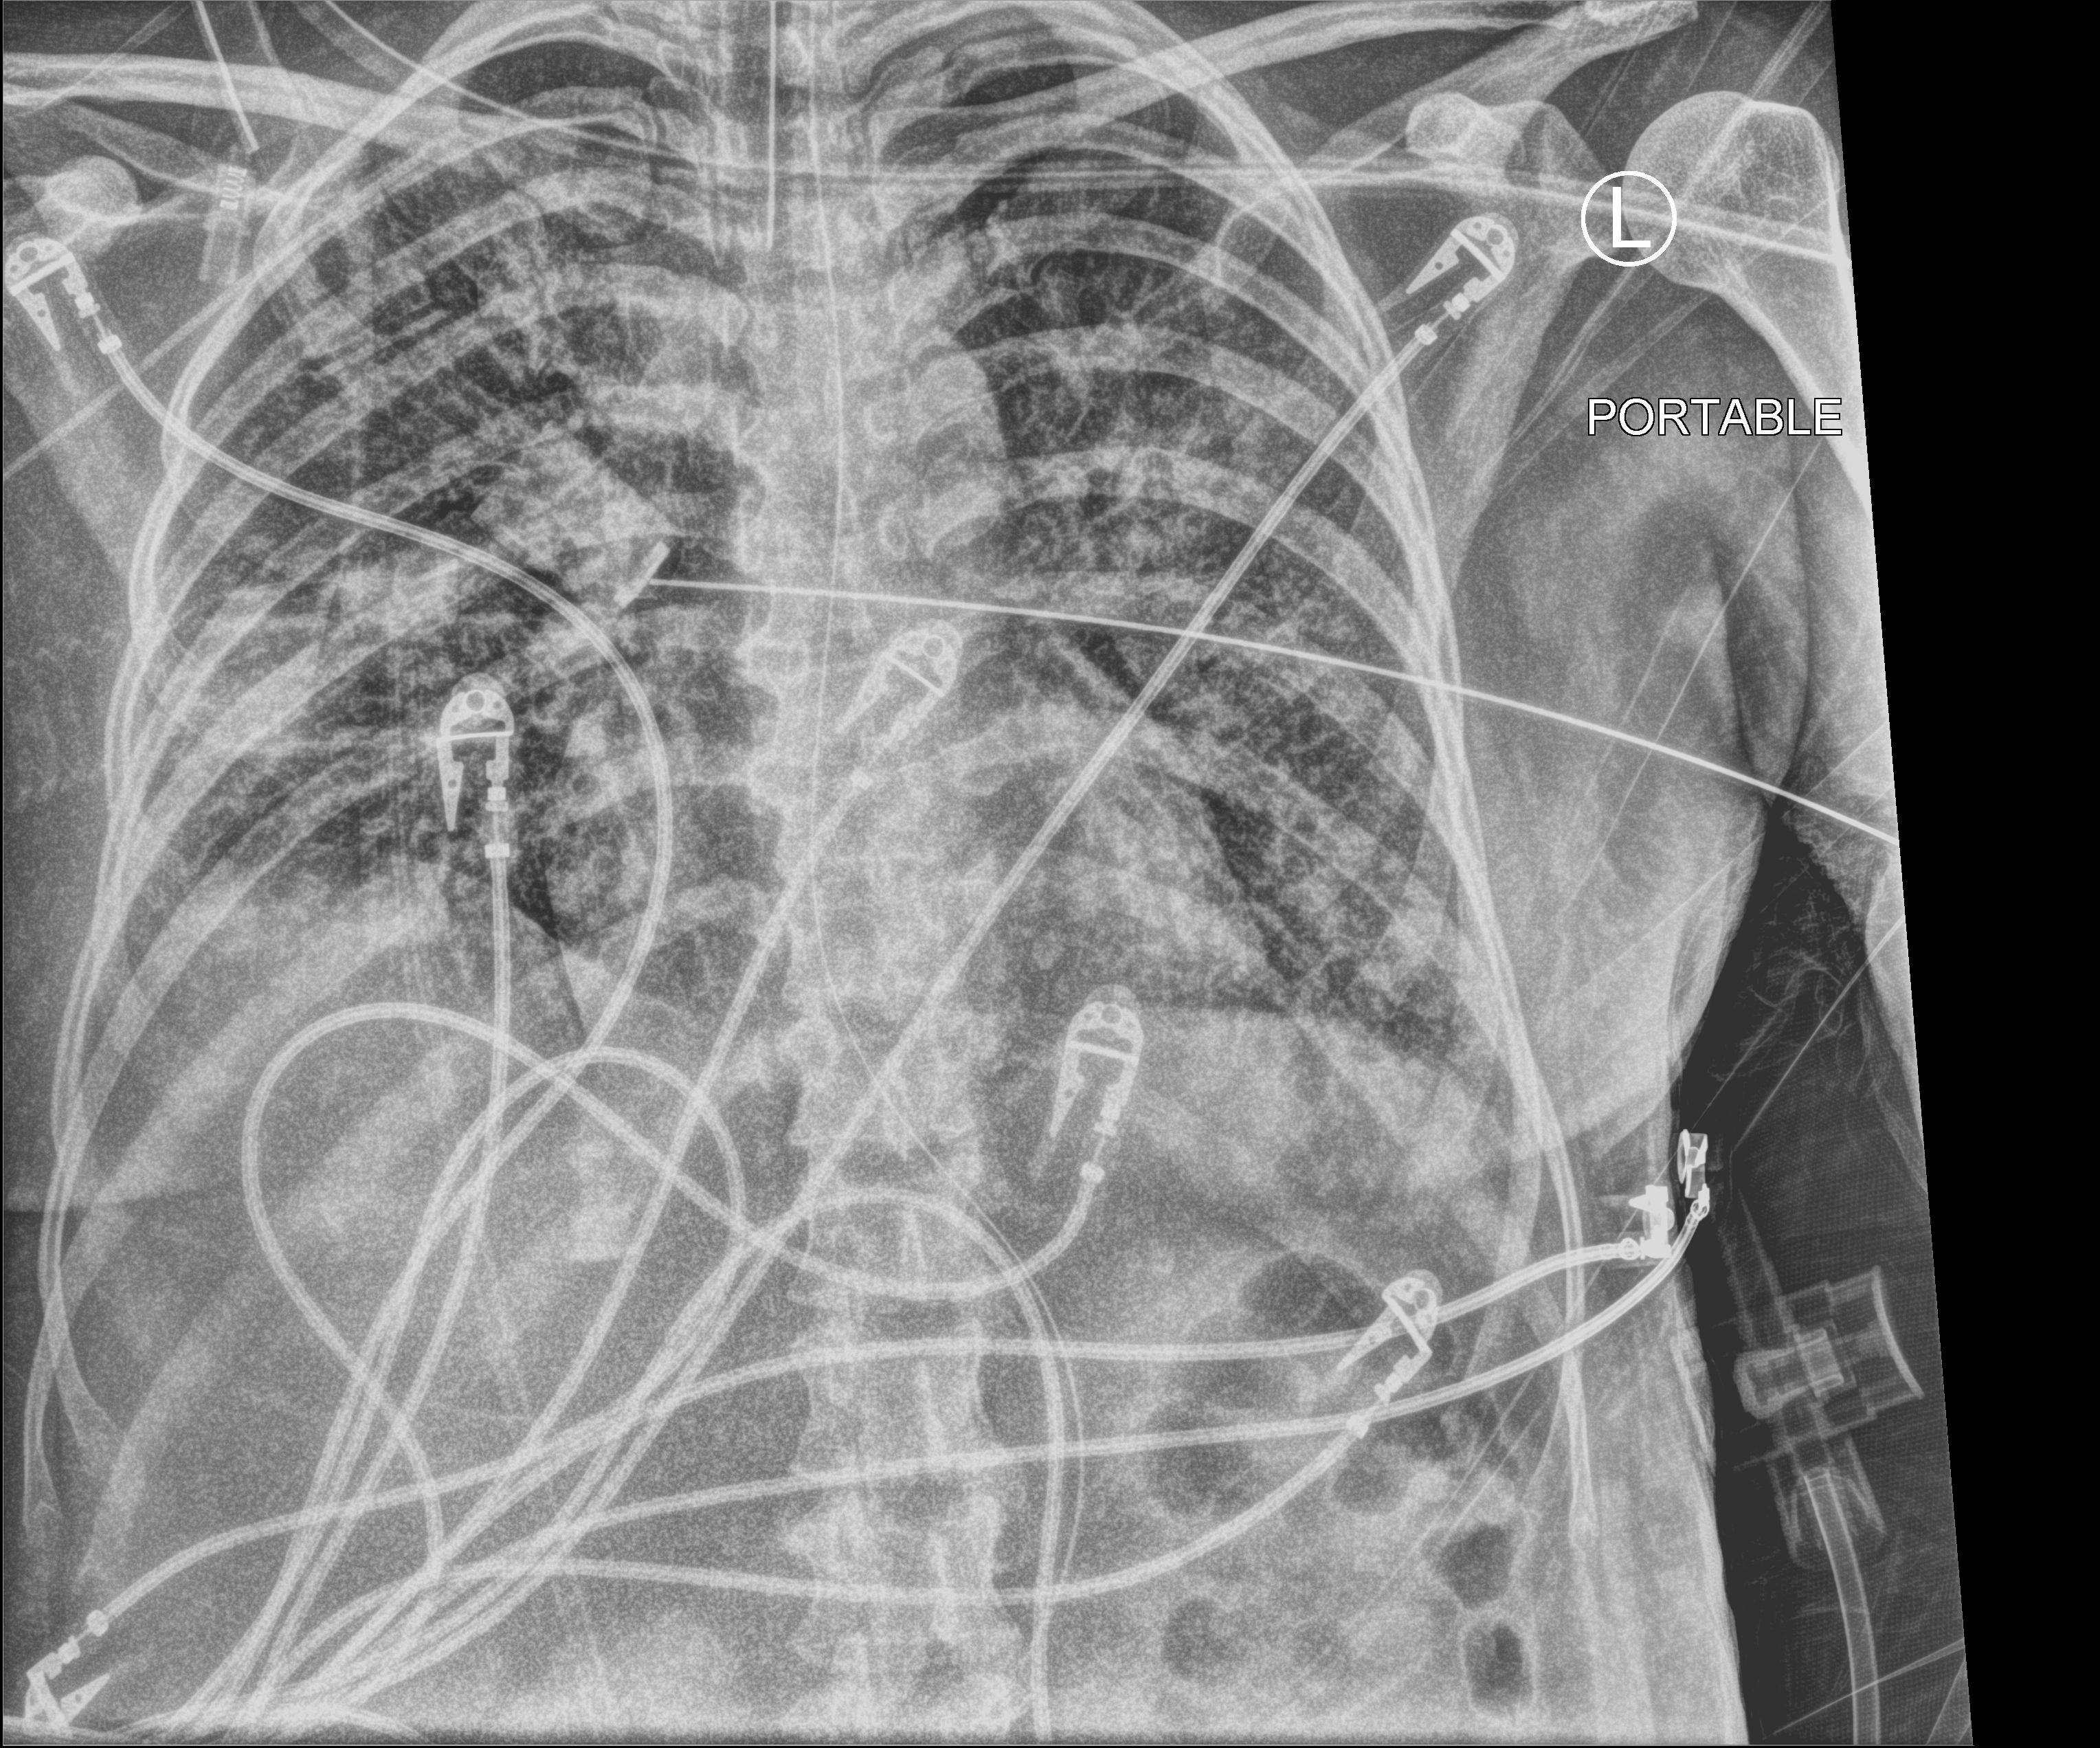
Bedside chest radiograph (computed radiography); anteroposterior (AP) projection. Female patient hospitalised with COVID-19, age 18–59 years.
Admission-level facts for this patient (not findings on this image; timing relative to this image not recorded):
- mechanically ventilated during this hospital stay: yes